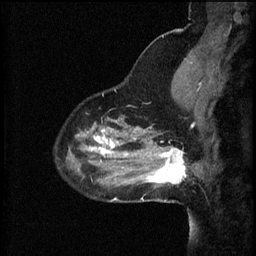
Breast MRI (dynamic contrast-enhanced), one sagittal slice; slice 16 of 60 in the series (ordered by position); 3 images stored at this slice position (order not interpretable as contrast timing); 1.5 T; TE 4.2 ms, TR 8.2 ms; 2 mm slice thickness; 256 × 256 image matrix, field of view 200 × 200 mm. Patient: female, 37 years.
Annotated regions visible in this slice (semi-automatic segmentation, software-assisted and operator-edited):
- analysis volume of interest (the breast-tissue region the enhancement analysis was run in; not a lesion): bounding box <148,140,193,187> (left, top, right, bottom; pixels)
- tumour enhancement mask (voxels above the 70 % enhancement threshold inside the analysis volume of interest): <148,148,187,185>